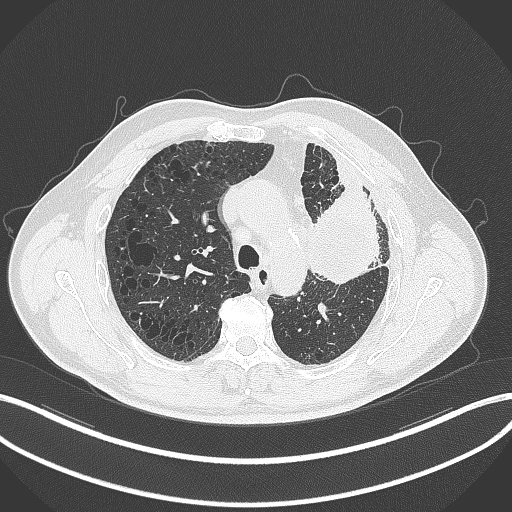
Chest CT, one axial slice. Slice 221 of 297 in the series (ordered by position). Reconstruction kernel B70f. 120 kVp. Lung window (W 1500 / L -600 HU). 512 × 512 image matrix, field of view 400 × 400 mm. Patient: male, 68 years. From the clinical record (not read from this slice): clinical TNM (as recorded): T3 N3 M1.
Annotated regions visible in this slice (bounding box drawn by a radiologist):
- lung tumour (recorded histology: adenocarcinoma): box from (x=308, y=183) to (x=390, y=291) px